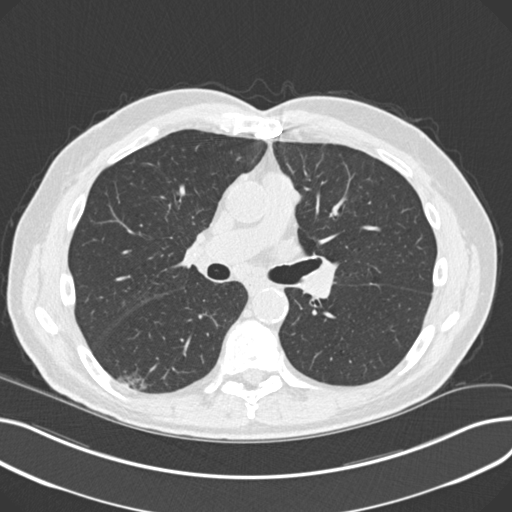
Low-dose screening chest CT, one axial slice. Lung window (W 1500 / L -600 HU). 512 × 512 image matrix, field of view 372 × 372 mm.
Outlined on this slice (manually delineated by an expert):
- lesion 1 (nodule, lower lobe of right lung): bounding box <118,368,148,390> (left, top, right, bottom; pixels)